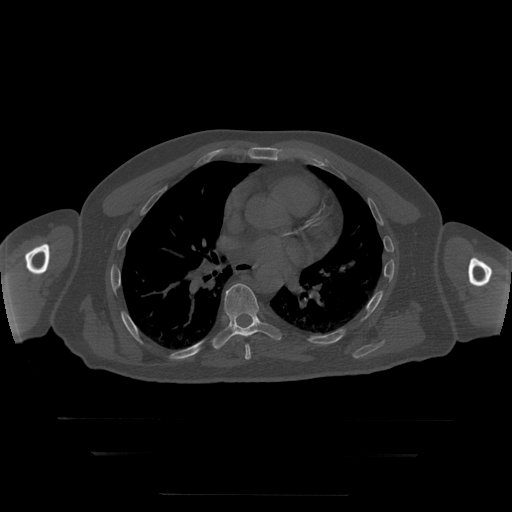
CT including the spine, one axial slice; position 170 of 397 along the scan axis; 120 kVp; bone window (W 1800 / L 400 HU); 1.25 mm slice thickness; 512 × 512 image matrix, field of view 510 × 510 mm. Patient age 73 years. From the clinical record (not read from this slice): primary cancer: prostate.
Structures marked on this image (semi-automatically segmented with operator editing):
- T7 vertebra: bounding box <245,345,251,360> (left, top, right, bottom; pixels)
- T8 vertebra: <212,284,282,350>